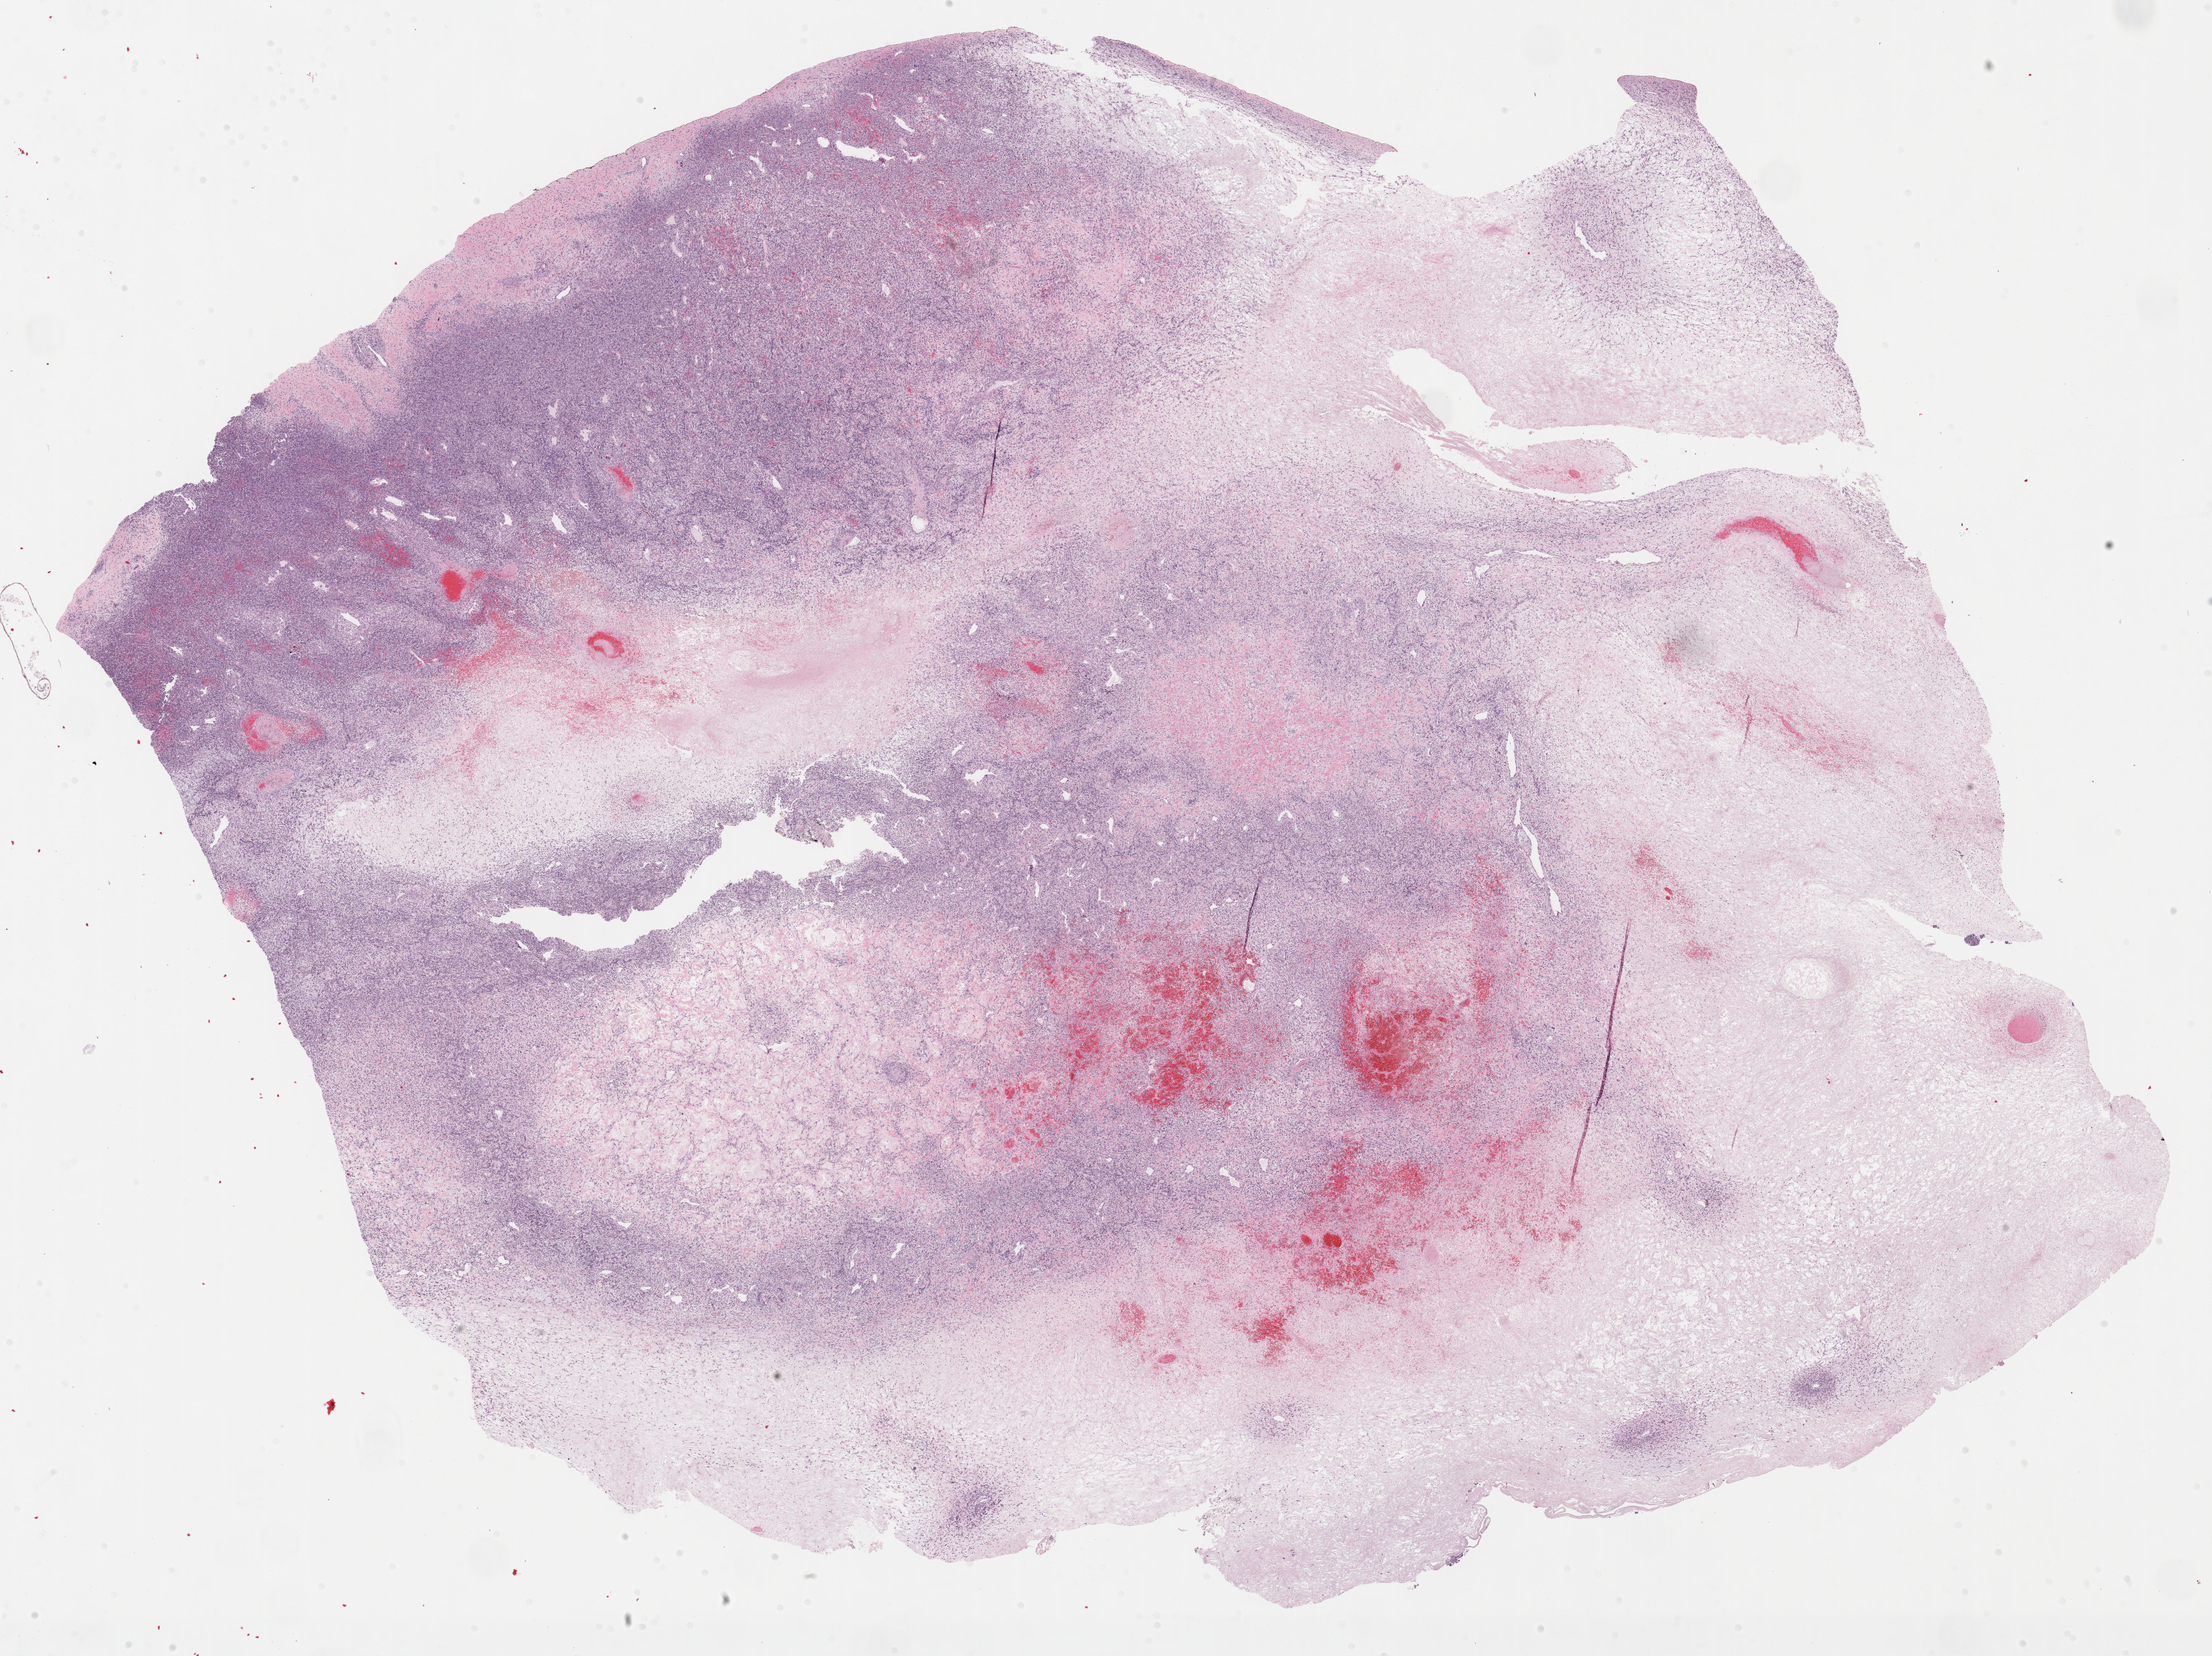
Digitized H&E-stained tissue section (whole slide) — low-resolution overview of the scanned area, about 26.7 x 20.0 mm (slide scanned at 40x), formalin-fixed paraffin-embedded (FFPE) diagnostic section, retroperitoneum and peritoneum, primary tumour sample. Patient: female, age at initial diagnosis 80 years.
* pathologic diagnosis: Dedifferentiated liposarcoma (retroperitoneum)